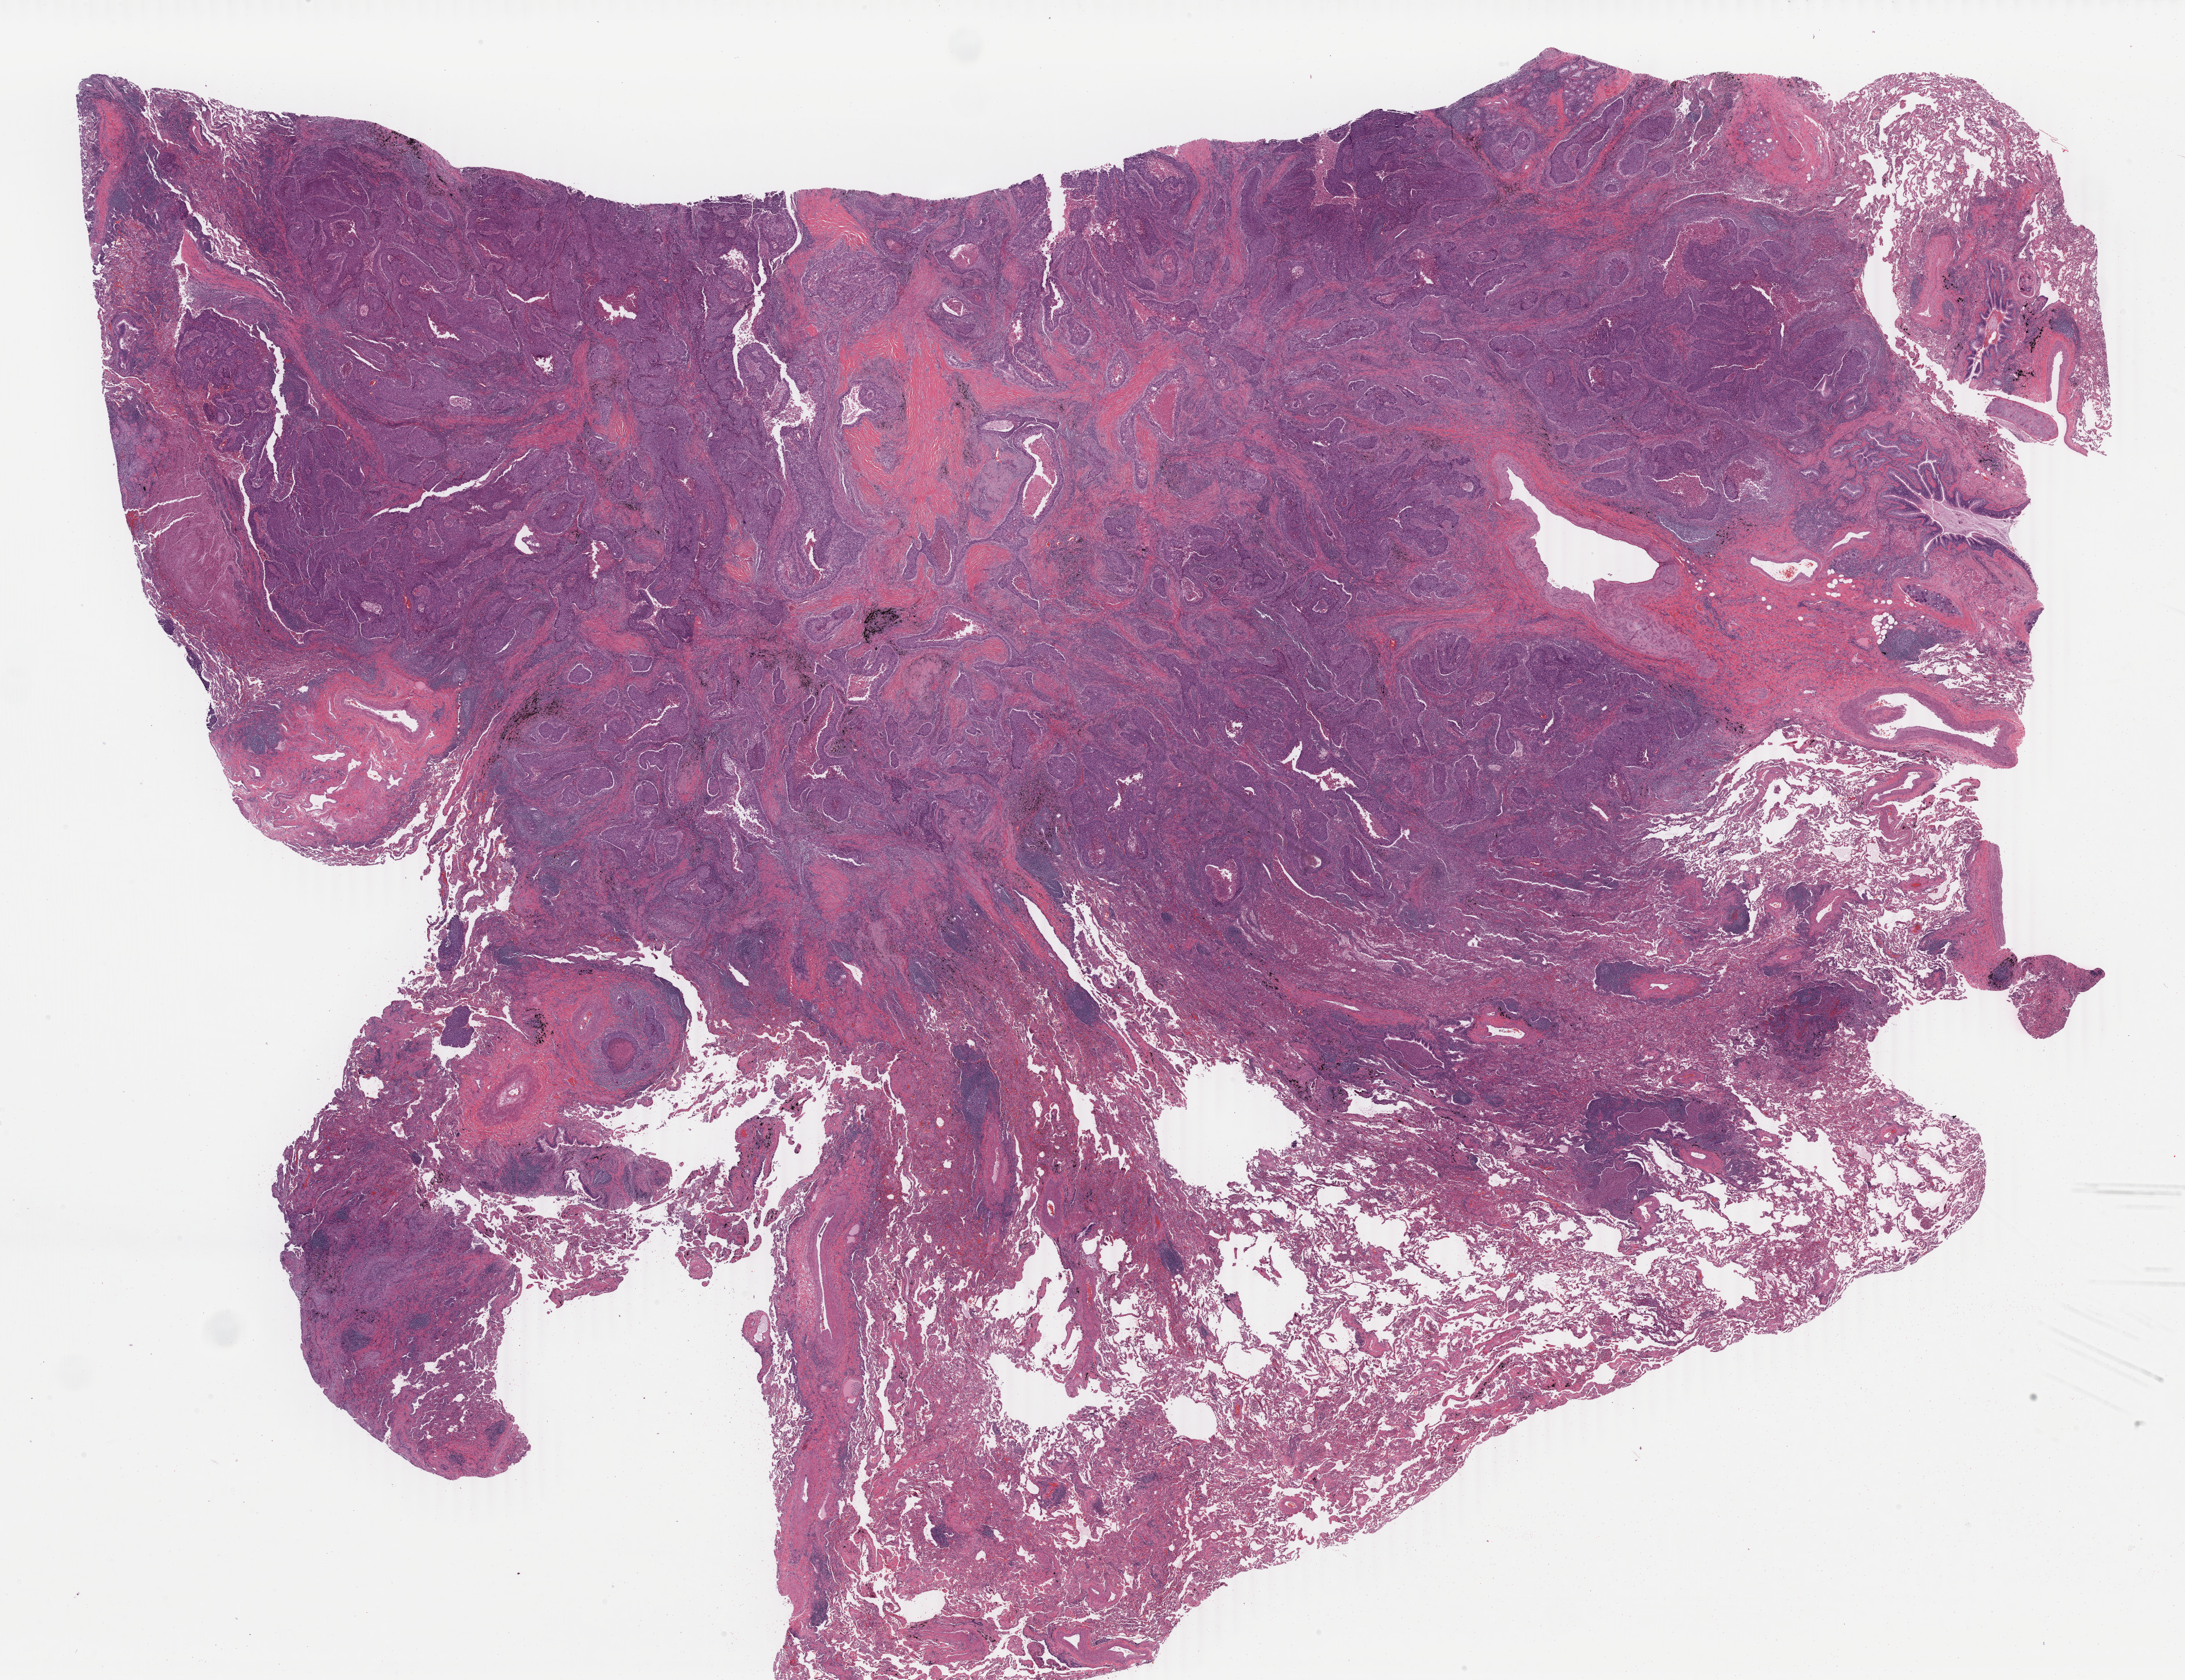
Hematoxylin and eosin (H&E) stained whole-slide image, shown as a low-resolution overview of the whole scanned area (about 30.0 x 23.1 mm, from a 40x scan). FFPE section. Lung, primary tumour sample. Male, age 65 years at initial diagnosis.
- AJCC pathologic stage: IIA (7th edition)
- diagnosis: Squamous cell carcinoma, NOS (upper lobe, lung)
- laterality: right